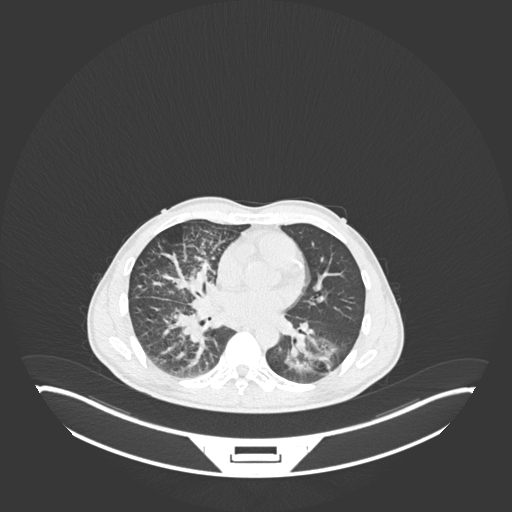
Chest CT, one axial slice; slice 111 of 237 in the series (ordered by position); lung window (W 1500 / L -600 HU); 1 mm slice thickness; 512 × 512 image matrix. Male patient, age 49 years. From the clinical record (not read from this slice): clinical TNM (as recorded): T2b N1 M0.
Annotated regions visible in this slice (bounding box drawn by a radiologist):
- lung tumour (recorded histology: adenocarcinoma): bounding box [x1, y1, x2, y2] px = [285, 328, 346, 384]